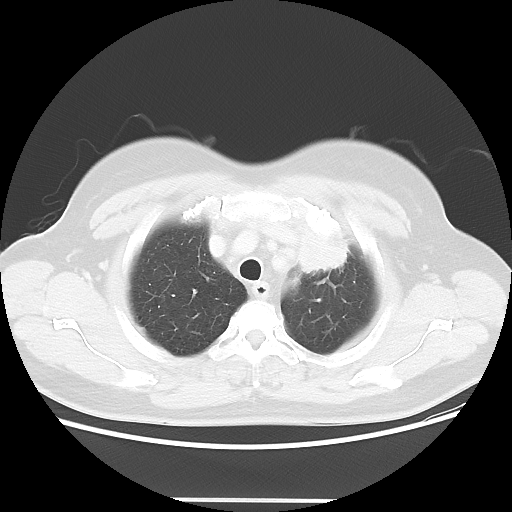
Chest CT, one axial slice. Slice 45 of 52 in the series (ordered by position). 120 kVp. Lung window (W 1500 / L -600 HU). 5 mm slice thickness. 512 × 512 image matrix. Patient: female, 52 years. Case-level facts recorded for this patient, not image findings: clinical TNM (as recorded): T2 N3 M0.
Structures marked on this image (bounding box drawn by a radiologist):
- lung tumour (recorded histology: adenocarcinoma): box from (x=290, y=214) to (x=355, y=277) px